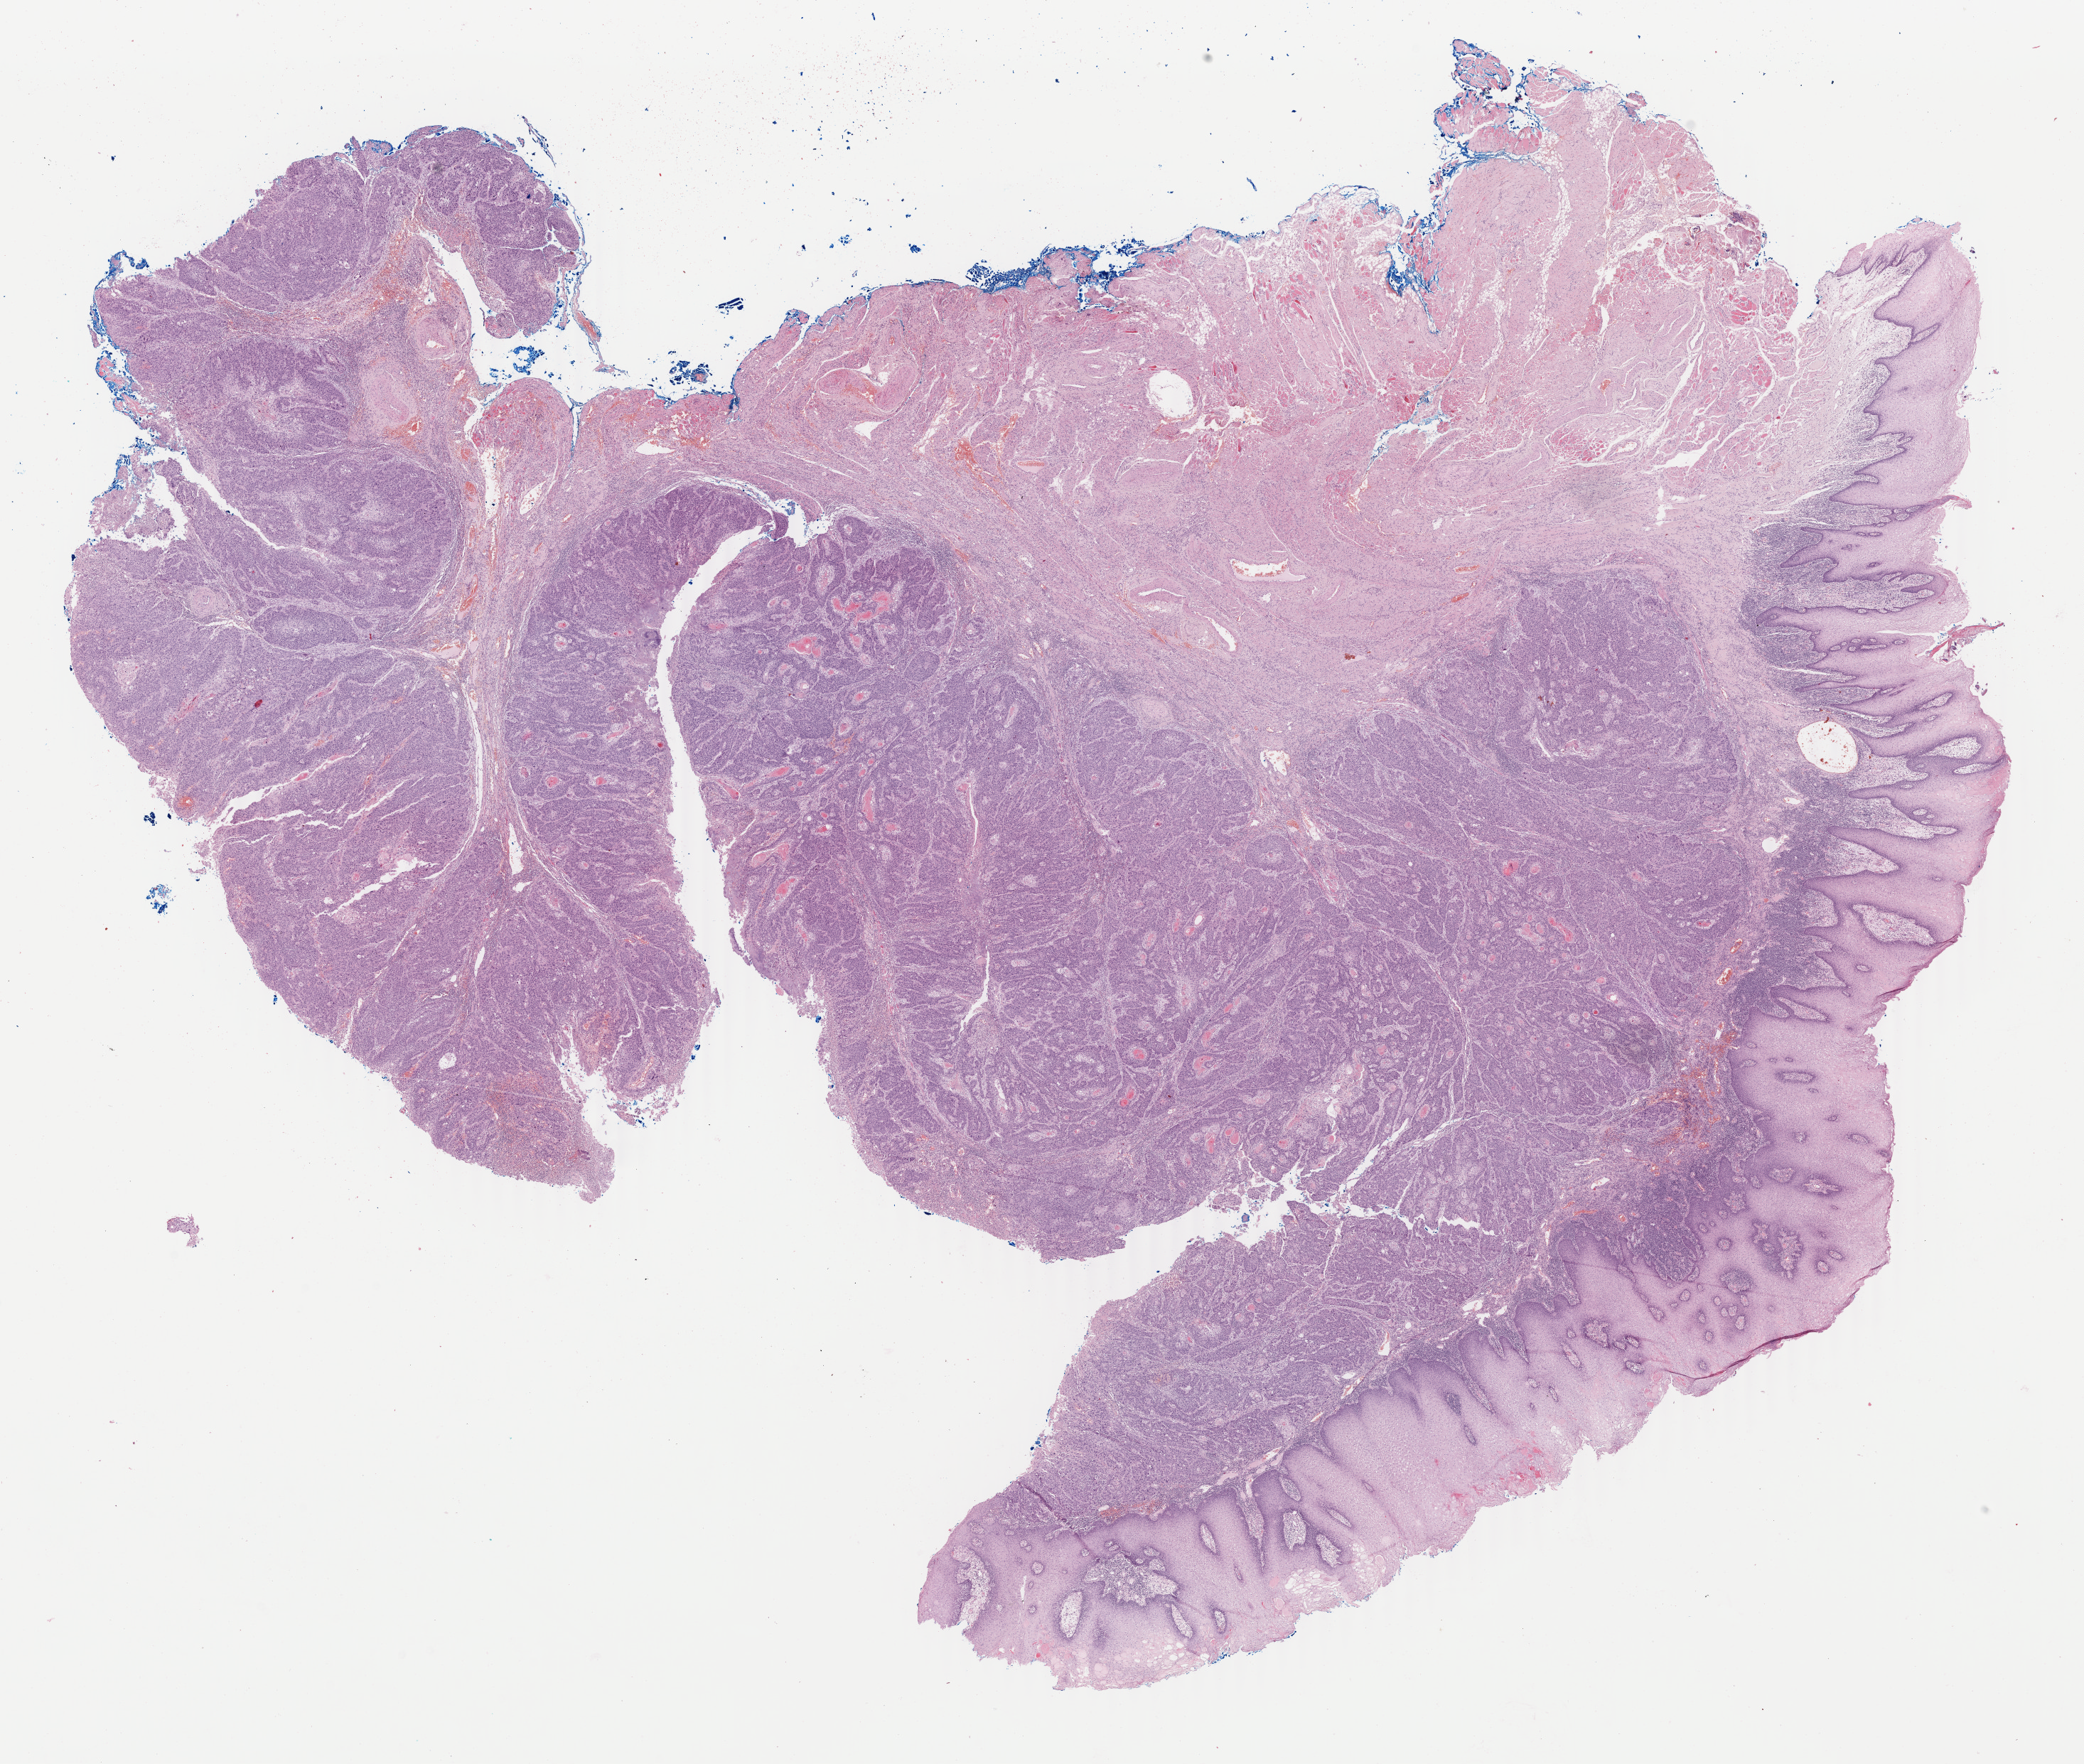
Hematoxylin and eosin (H&E) stained whole-slide image, whole scanned area (about 23.3 x 19.7 mm) shown as a low-resolution overview. FFPE section. Sample: primary tumour, head and neck. Male patient; age at initial diagnosis 50 years. Histologic grade: G2 (moderately differentiated).
Laterality: left. AJCC pathologic stage: II (7th edition). Diagnosis: Squamous cell carcinoma, NOS (tongue, NOS).